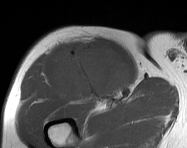
MRI of an extremity soft-tissue mass, one axial slice; slice 101 of 114 in the series (ordered by position); MR volume resampled by the dataset authors to the PET/CT grid (not the native acquisition matrix); 187 × 148 image matrix. Male patient. Case-level facts recorded for this patient, not image findings: histological type: pleiomorphic leiomyosarcoma; grade: intermediate; site of the primary tumour: right thigh.
Outlined on this slice (expert contour drawn on MRI and transferred to this co-registered scan by the dataset authors):
- gross tumour volume including surrounding oedema: box from (x=54, y=38) to (x=131, y=103) px
- gross tumour volume (mass): (x=57, y=38)–(x=131, y=103)